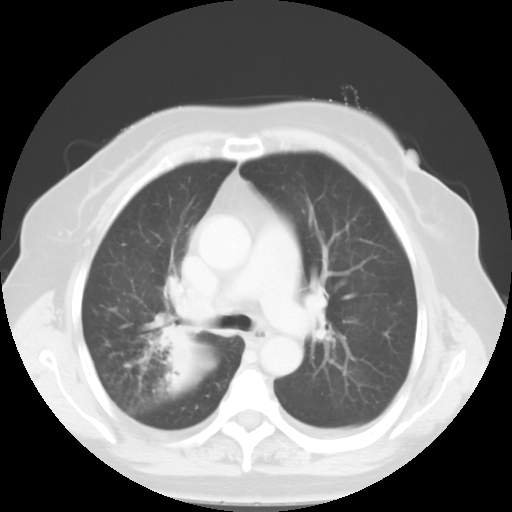
Chest CT, one axial slice; slice 34 of 52 in the series (ordered by position); lung window (W 1500 / L -600 HU); 5 mm slice thickness; 512 × 512 image matrix, field of view 333 × 333 mm. Patient: female, 81 years. From the clinical record (not read from this slice): clinical TNM (as recorded): T4 N3 M1b.
Outlined on this slice (rectangle marked by the reading radiologist):
- lung tumour (recorded histology: adenocarcinoma): bounding box [x1, y1, x2, y2] px = [151, 319, 204, 396]